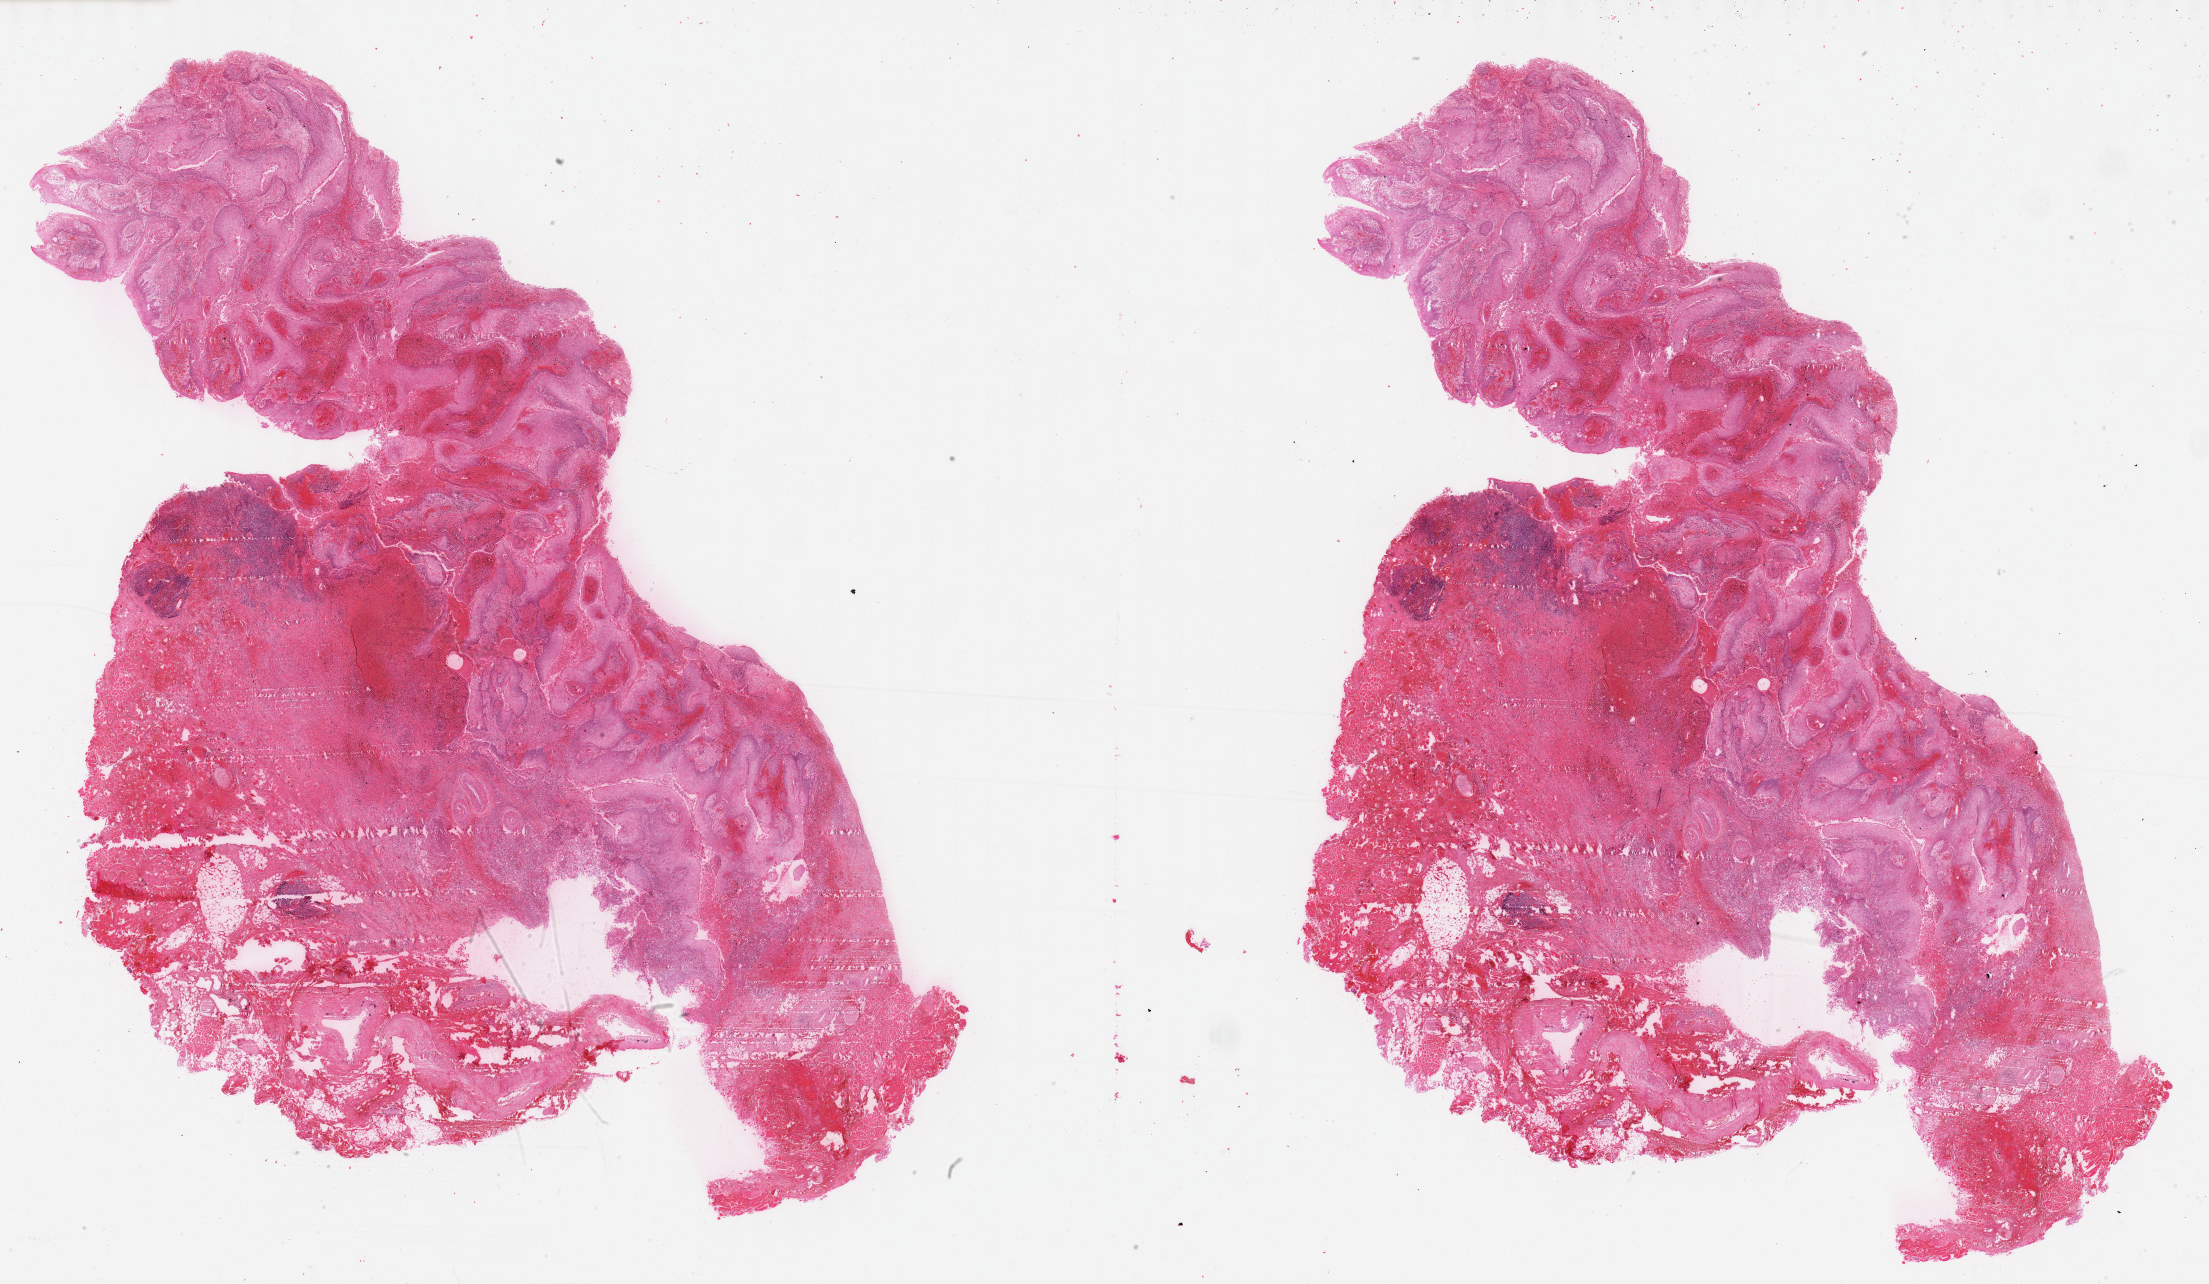
Whole-slide histology image, H&E-stained, whole scanned area (about 35.7 x 20.8 mm) shown as a low-resolution overview; FFPE section; head and neck, primary tumour sample. Patient: female, age at initial diagnosis 87 years. Histologic grade: G1 (well differentiated).
* AJCC pathologic stage: IVA (5th edition)
* laterality: right
* histologic diagnosis: Squamous cell carcinoma, NOS (mouth, NOS)